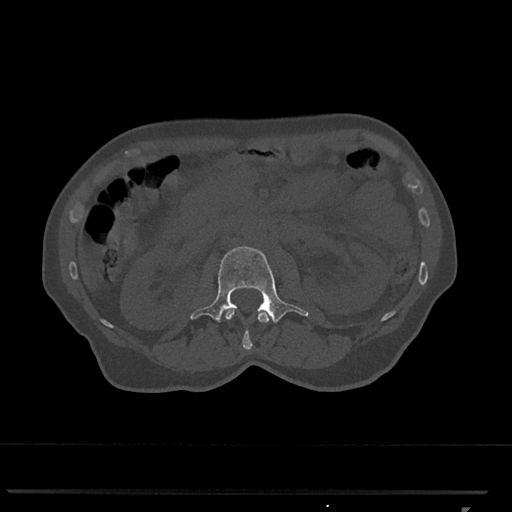
CT including the spine, one axial slice; position 354 of 793 along the scan axis; reconstruction kernel Br40s/3; 120 kVp; bone window (W 1800 / L 400 HU); 512 × 512 image matrix, field of view 380 × 380 mm. Patient: female, 62 years. From the clinical record (not read from this slice): primary cancer: renal.
Outlined on this slice (semi-automatically segmented with operator editing):
- L1 vertebra: bounding box (x1, y1, x2, y2) in pixels: (225, 309, 270, 350)
- L2 vertebra: (190, 246, 309, 323)